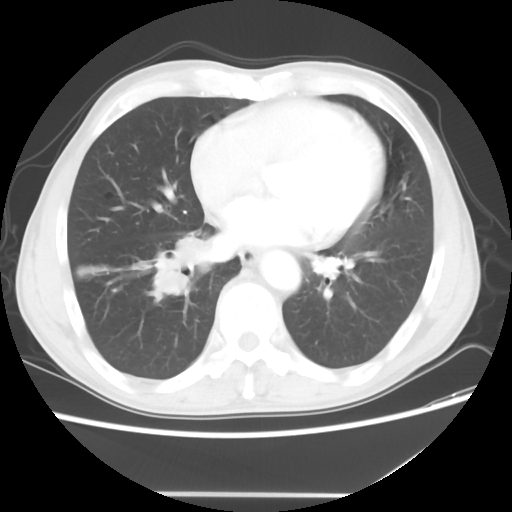
Chest CT, one axial slice. Slice 20 of 56 in the series (ordered by position). 120 kVp. Lung window (W 1500 / L -600 HU). 512 × 512 image matrix, field of view 344 × 344 mm. Patient: male, 65 years. From the clinical record (not read from this slice): clinical TNM (as recorded): T1c N3 M0; histopathological grade: G3.
Structures marked on this image (bounding box drawn by a radiologist):
- lung tumour (recorded histology: small cell carcinoma): bounding box [x1, y1, x2, y2] px = [153, 231, 213, 303]